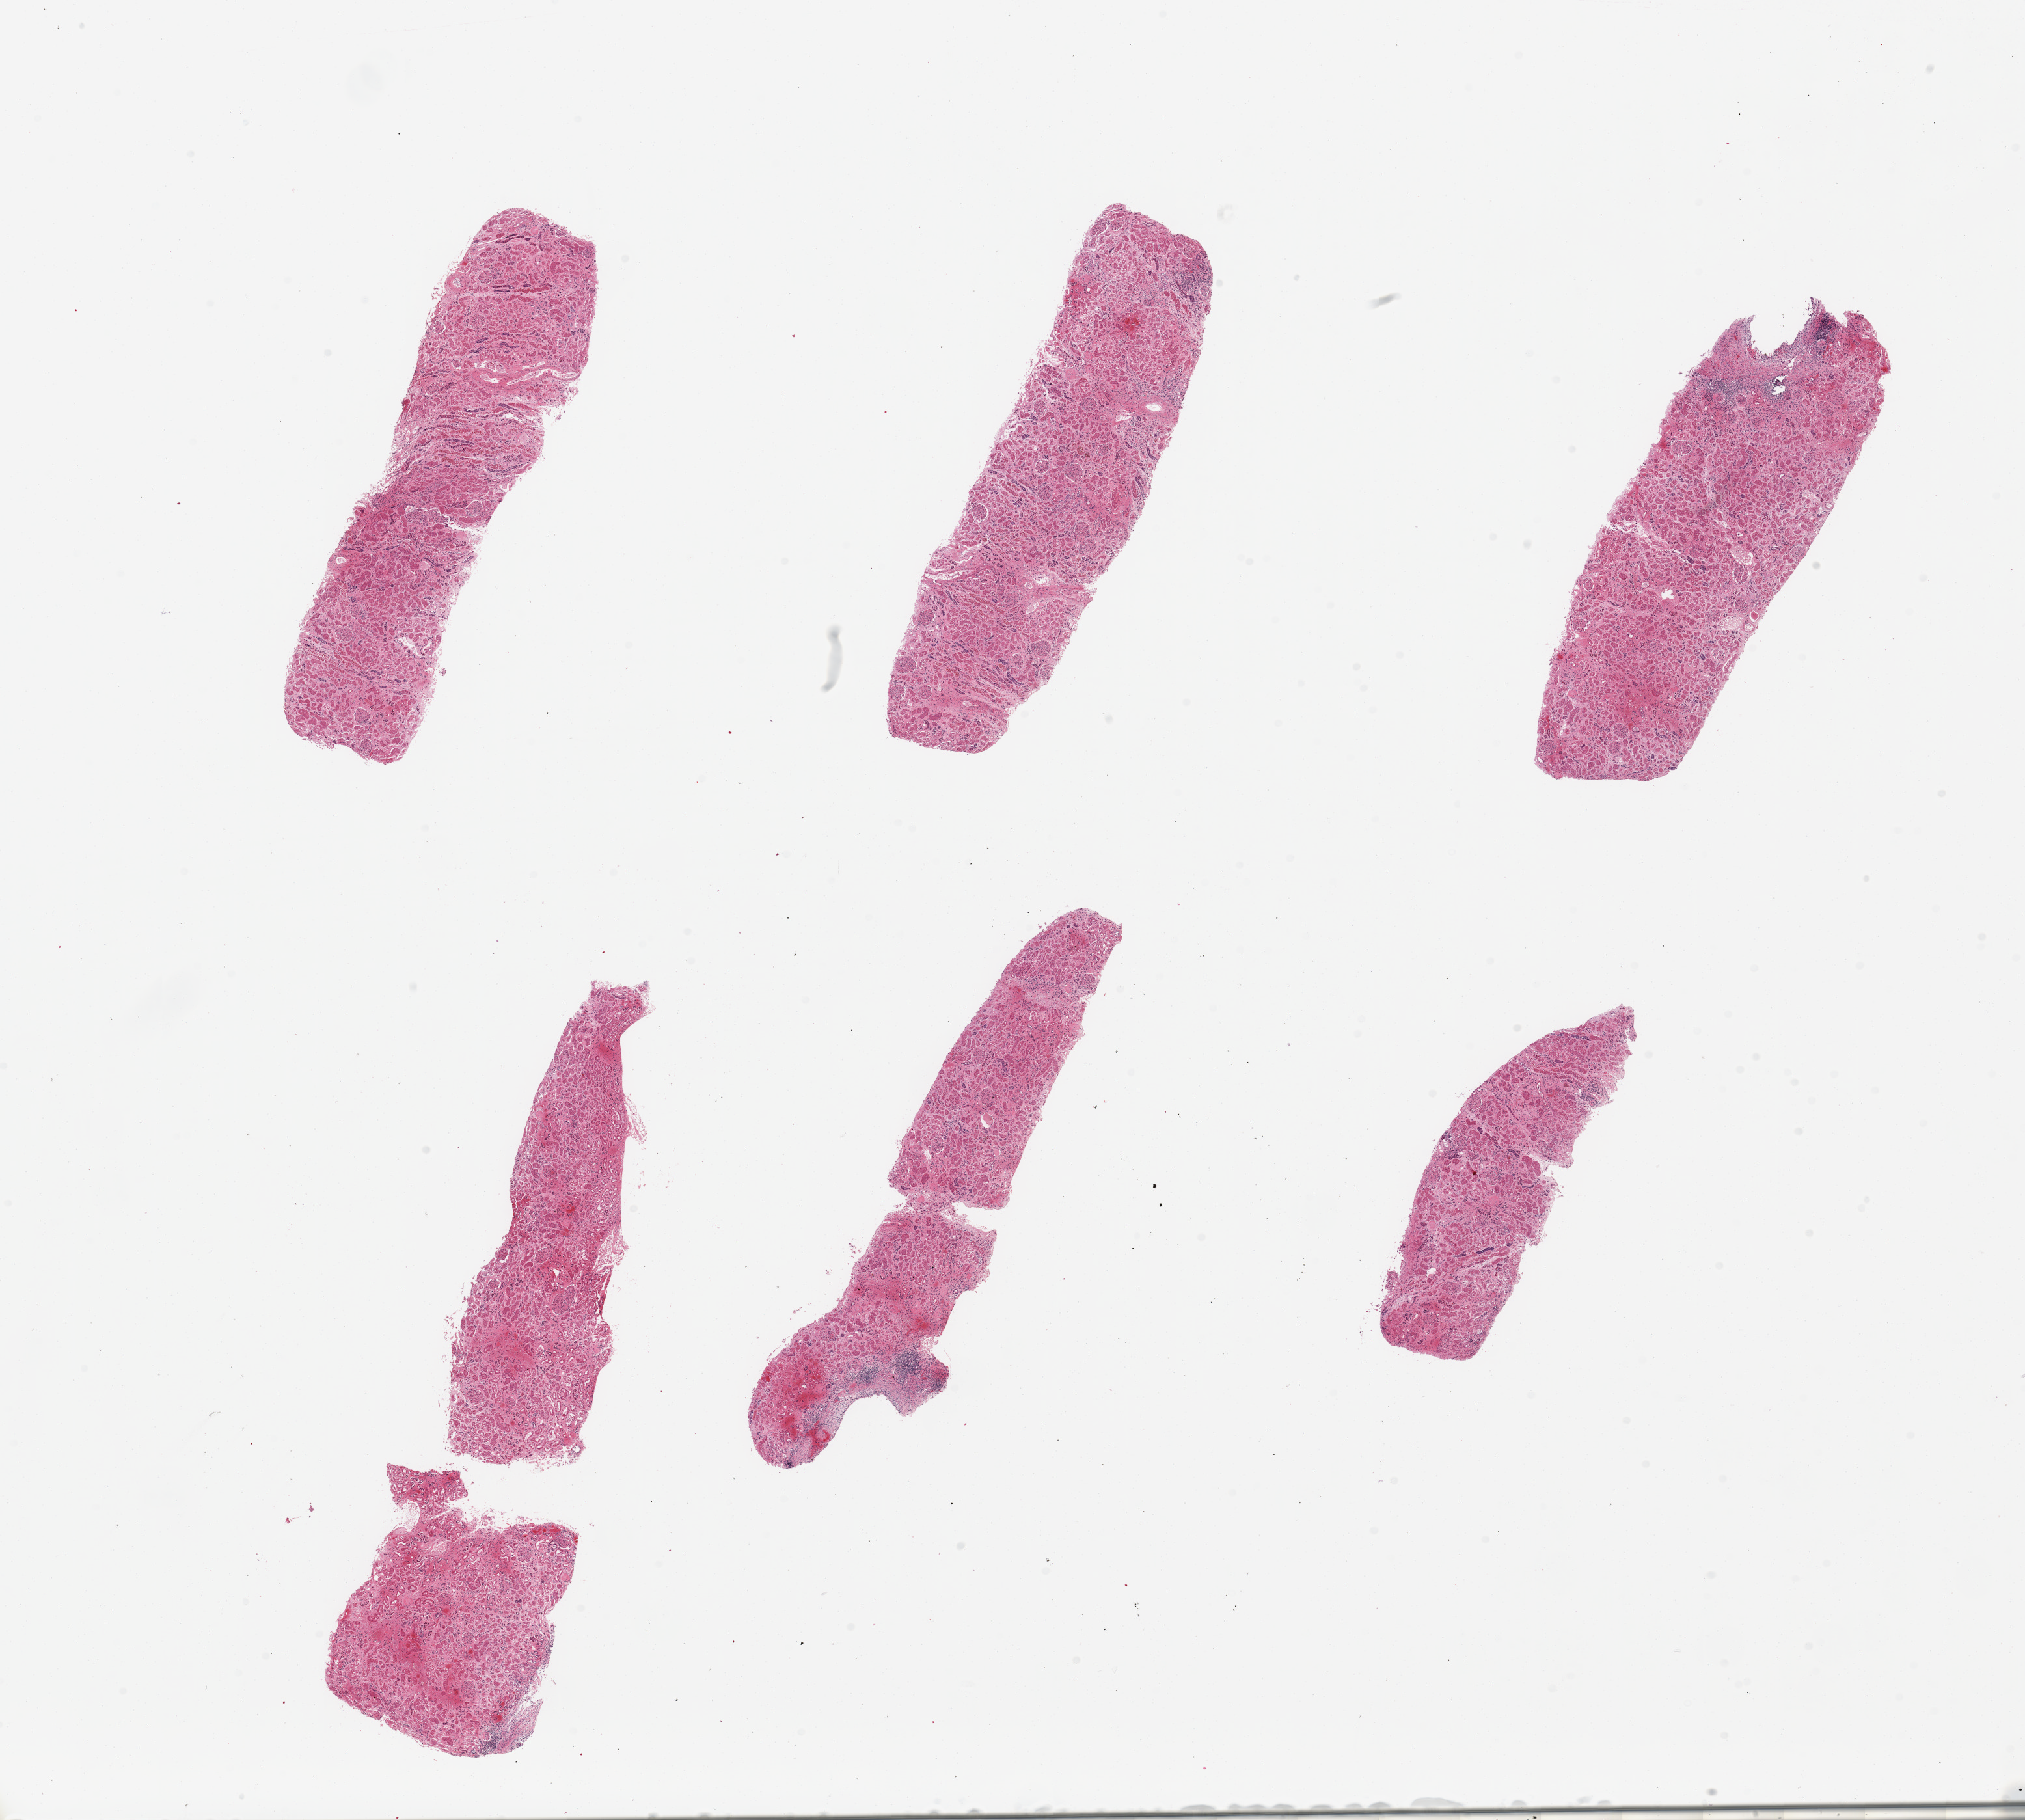
Digitized hematoxylin and eosin (H&E)-stained section, brightfield — low-resolution overview of the scanned area, about 24.6 x 22.1 mm (acquisition: 20x scan), PAXgene-fixed, paraffin-embedded tissue, target tissue: renal cortex, tissue donor sample. Donor sex: female.
Pathologist's review note for this sample: 6 pieces, glomeruli present; tubules with advanced autolysis.